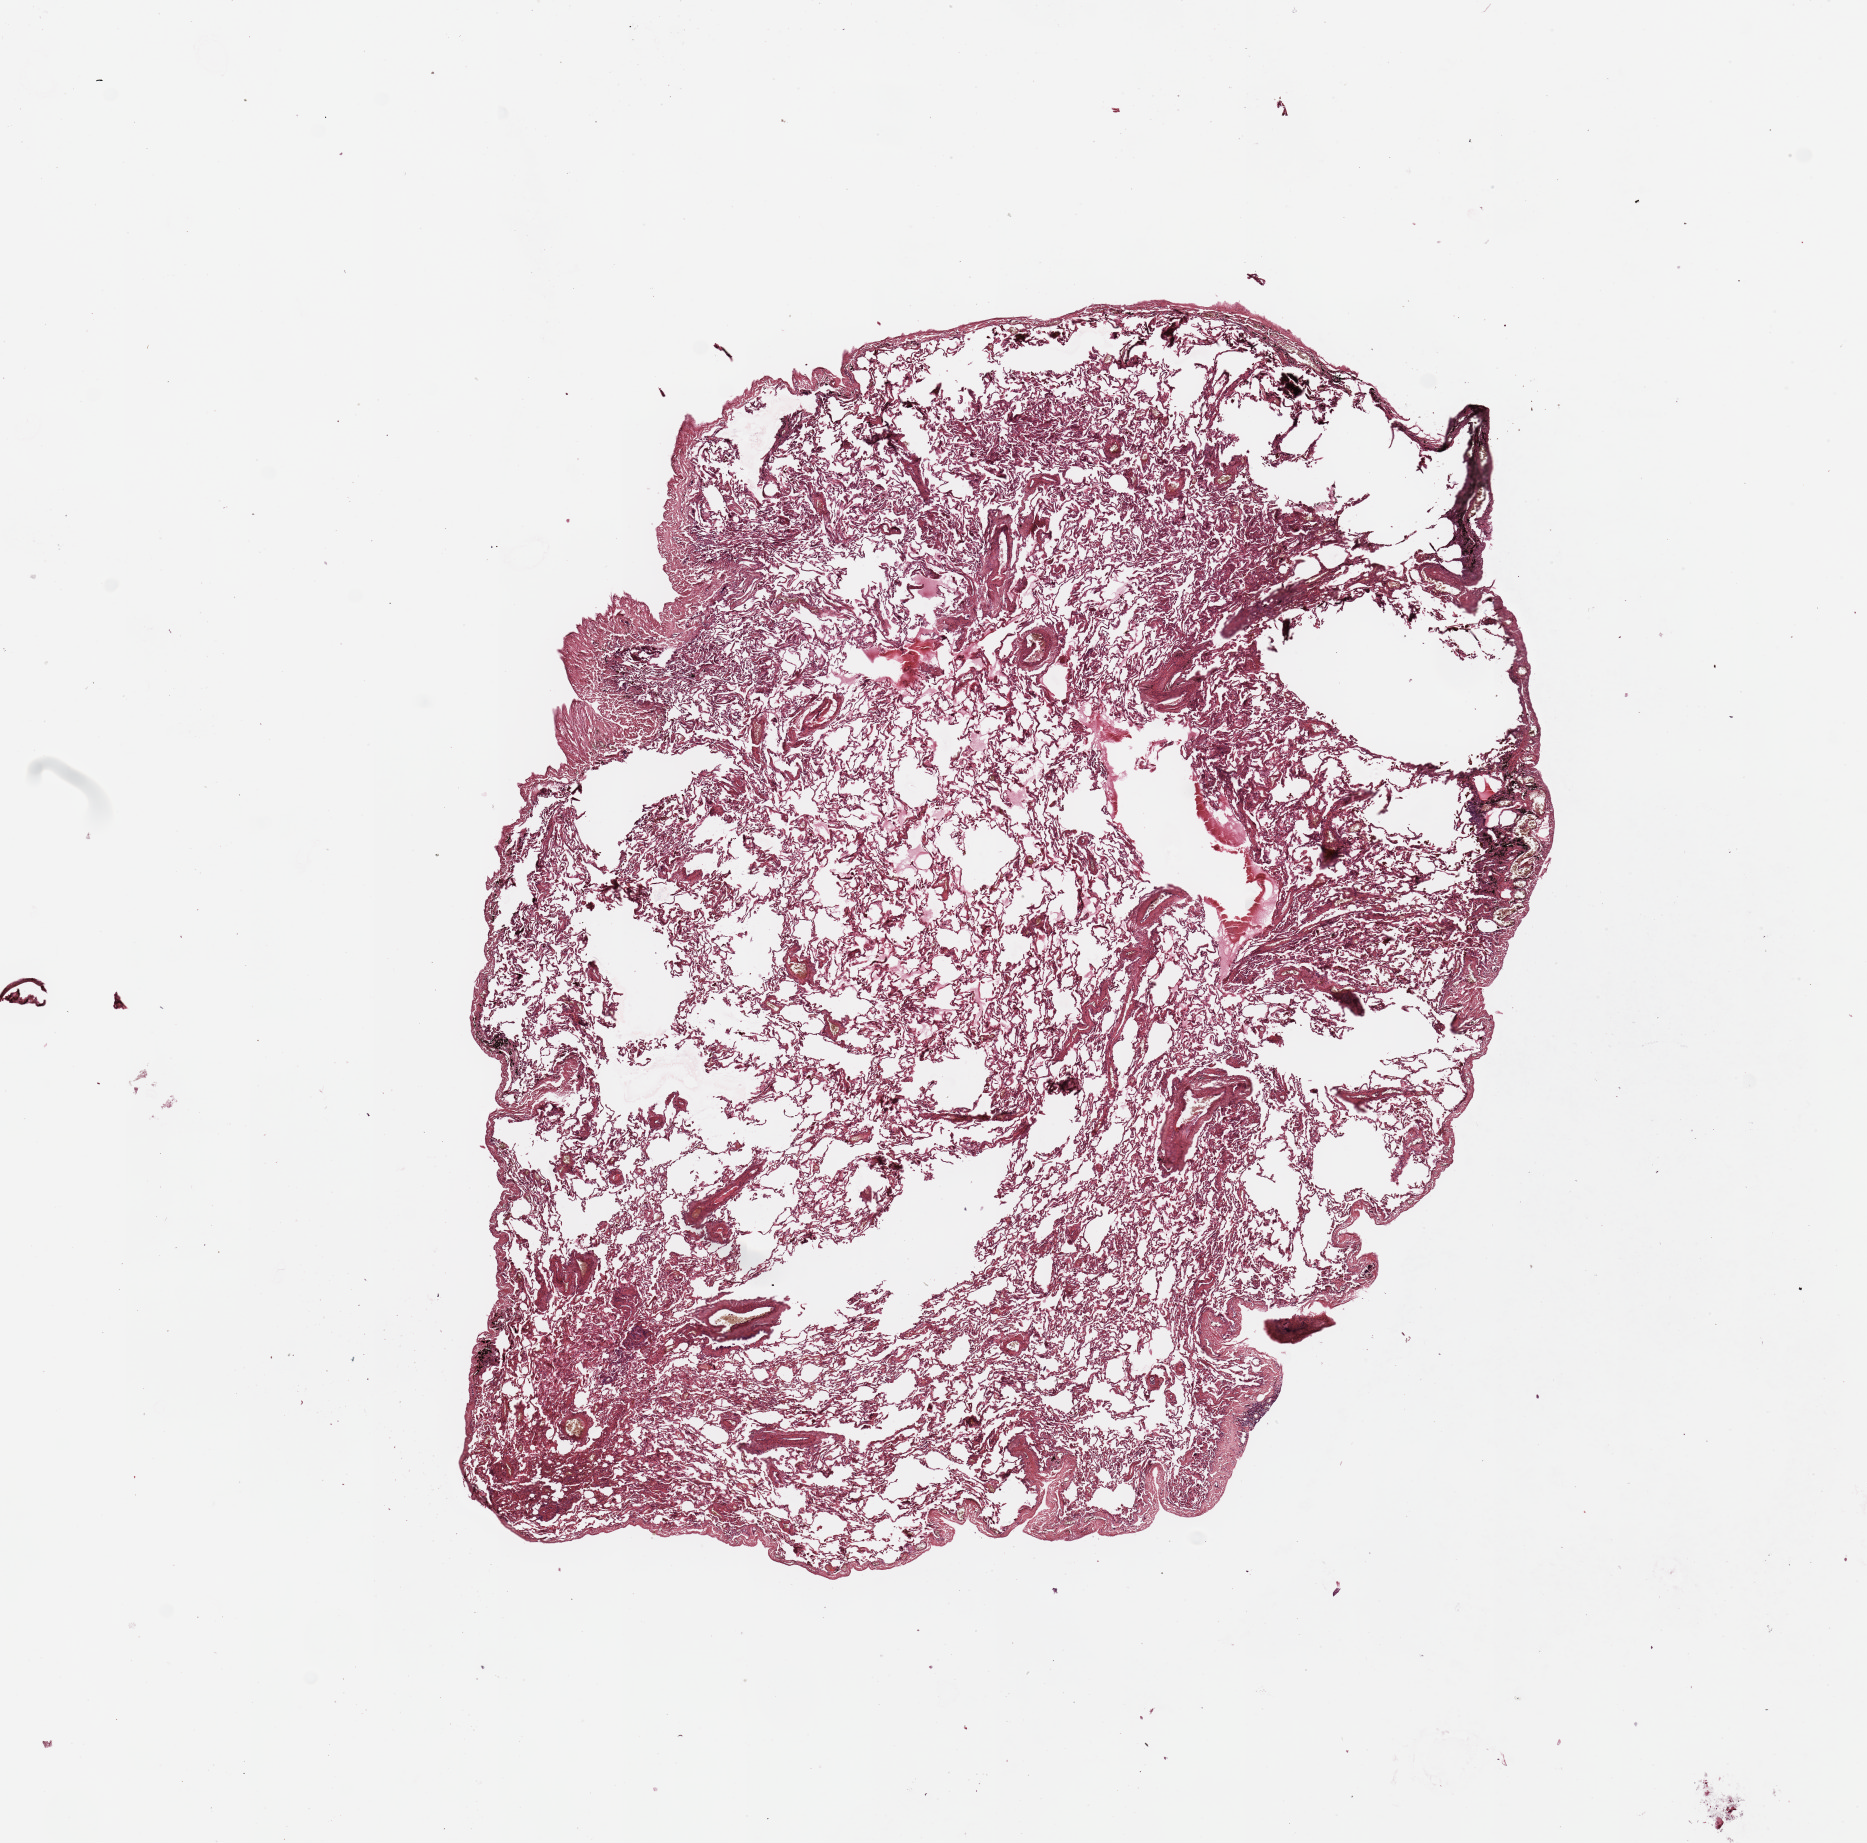
H&E whole-slide image, low-resolution overview of the scanned area, about 14.8 x 14.6 mm (slide scanned at 20x), normal (non-tumour) tissue sample, sampled site: lung. 63-year-old male patient.
This section: normal (non-tumour) tissue from the same patient. Patient diagnosis: Adenocarcinoma, NOS.